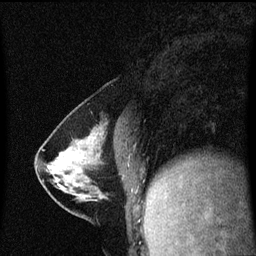
Breast MRI (dynamic contrast-enhanced), one sagittal slice. Position 23 of 60 along the scan axis. Dynamic contrast-enhanced series, image 2 of 3 at this slice position (ordered by acquisition). 1.5 T. TE 4.2 ms, TR 8.4 ms. 2 mm slice thickness. 256 × 256 image matrix, field of view 200 × 200 mm. Female patient, age 40 years. Case-level facts recorded for this patient, not image findings: setting: breast cancer imaged before/during neoadjuvant chemotherapy; receptor status: triple-negative.
Annotated regions visible in this slice (semi-automatic segmentation, software-assisted and operator-edited):
- analysis volume of interest (the breast-tissue region the enhancement analysis was run in; not a lesion): bounding box <35,142,108,199> (left, top, right, bottom; pixels)
- tumour enhancement mask (voxels above the 70 % enhancement threshold inside the analysis volume of interest): <59,160,62,163>